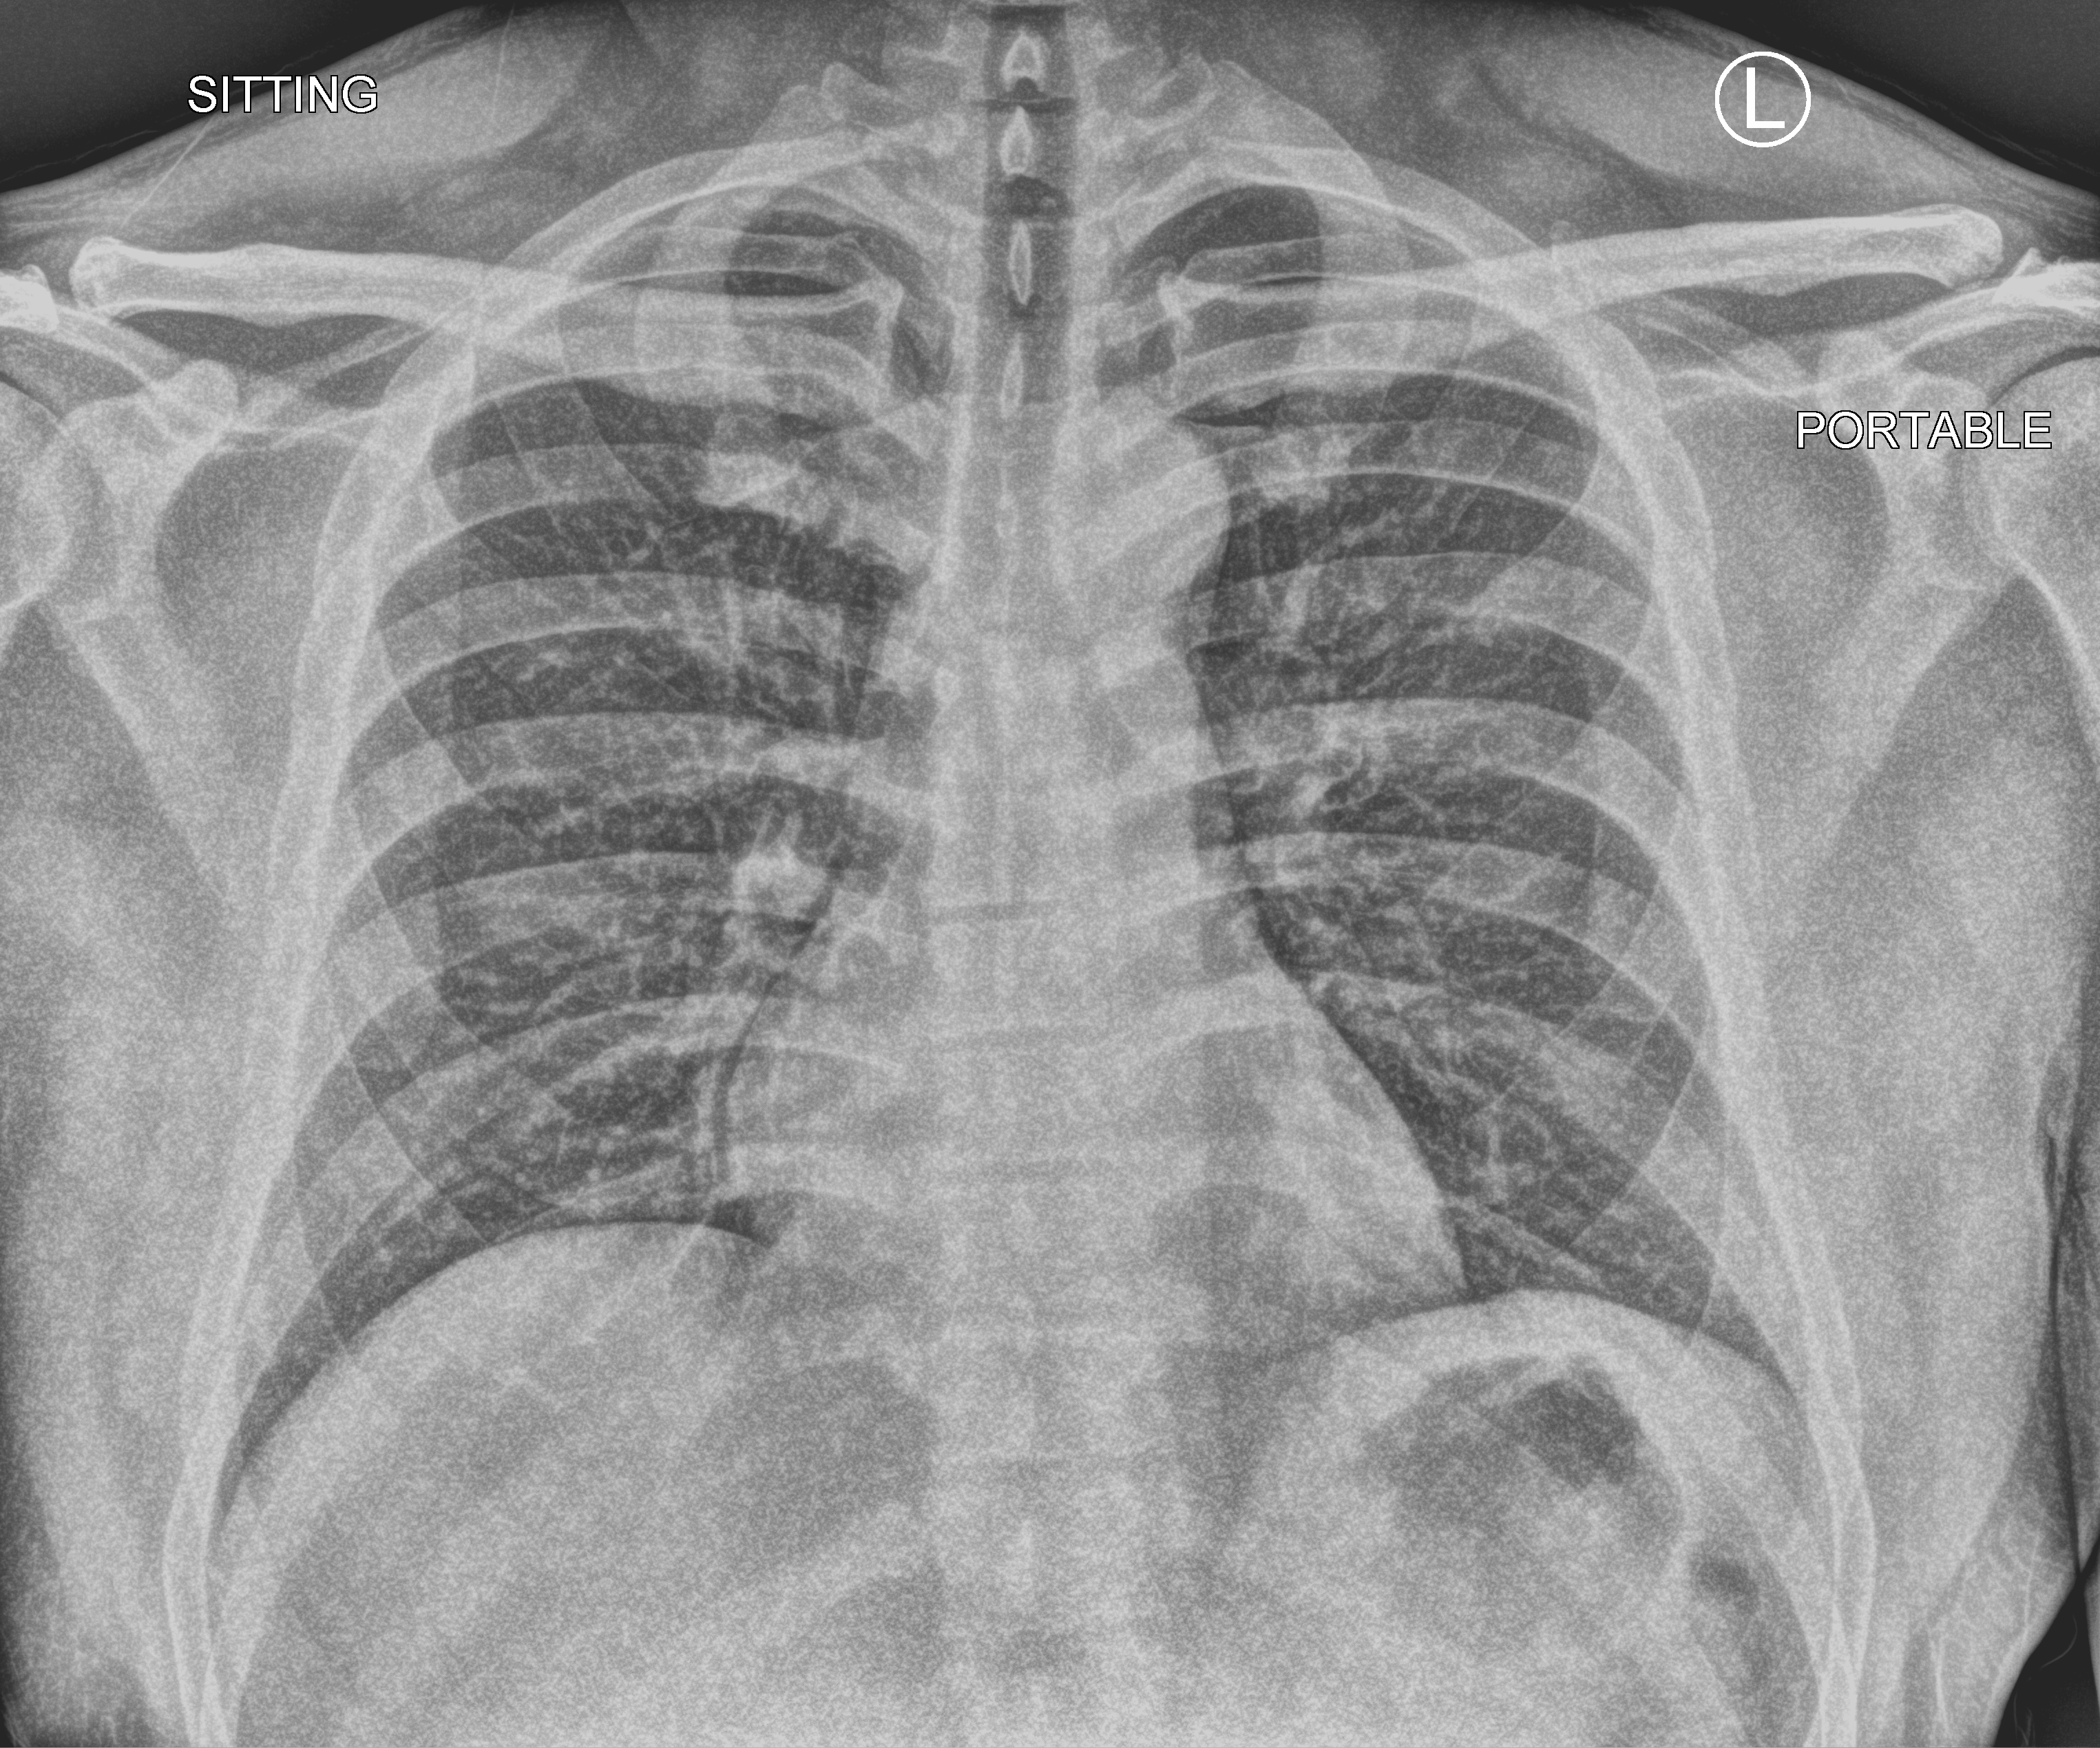
Portable chest radiograph; anteroposterior (AP) projection. Patient hospitalised with COVID-19; male, aged 18–59 years.
Hospital-stay facts (about this admission, not read from this image; timing relative to this image not recorded):
- admitted to intensive care during this hospital stay: no
- chronic kidney disease (admission record): no
- diabetes (admission record): no